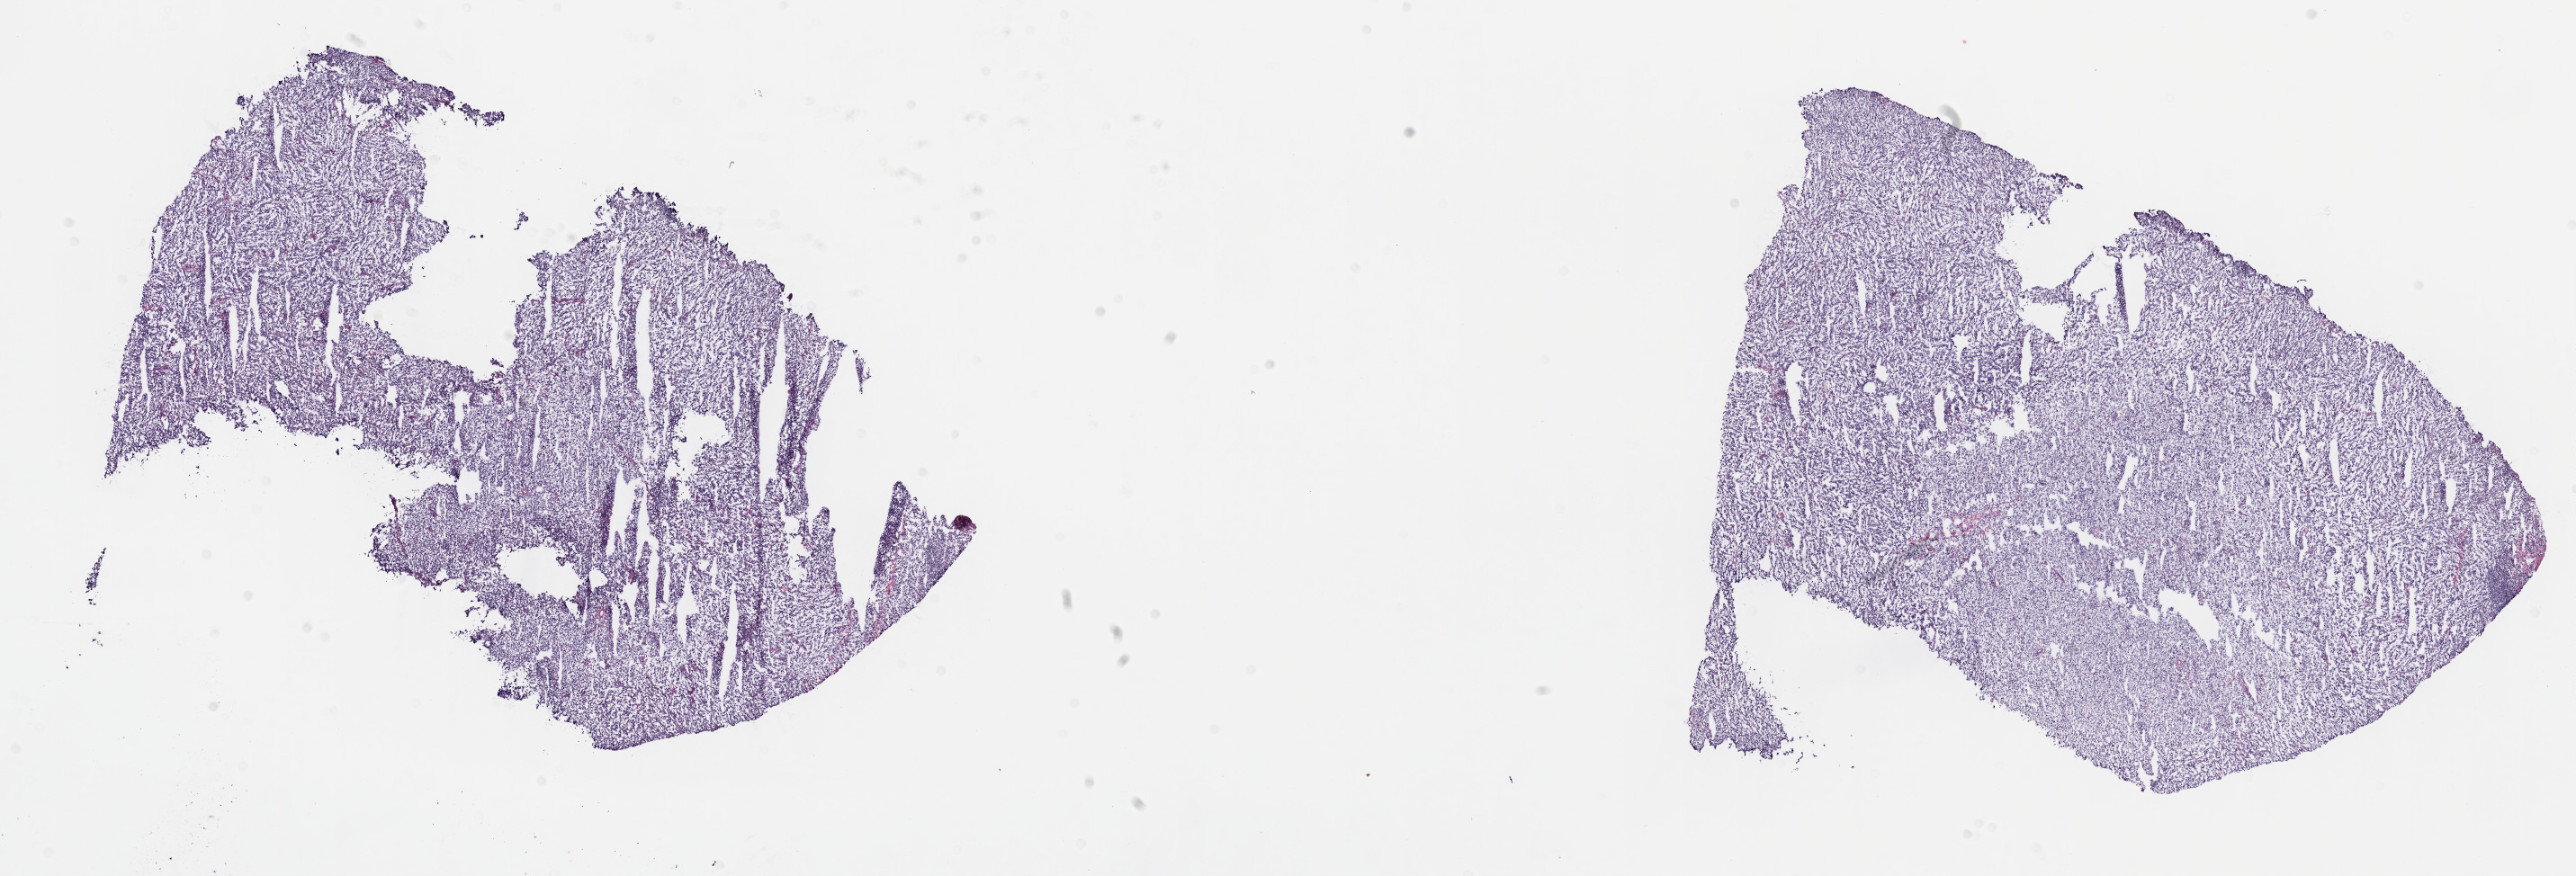
Whole-slide histology image, Hematoxylin and eosin (H&E) stained — low-resolution overview of the scanned area, about 23.2 x 7.9 mm, frozen section from the top of the tissue portion, sample: primary tumour, testis. Male patient; age at initial diagnosis 30 years. Composition of this section per pathologist review: tumour cells 90%, tumour nuclei 90%, normal cells 0%, stromal cells 10%, necrosis 0%. Infiltration values recorded for this section: lymphocyte infiltration 60%, monocyte infiltration 20%, neutrophil infiltration 10%.
TNM: T1 N0 M0. Pathologic diagnosis: Seminoma, NOS. AJCC pathologic stage: I.